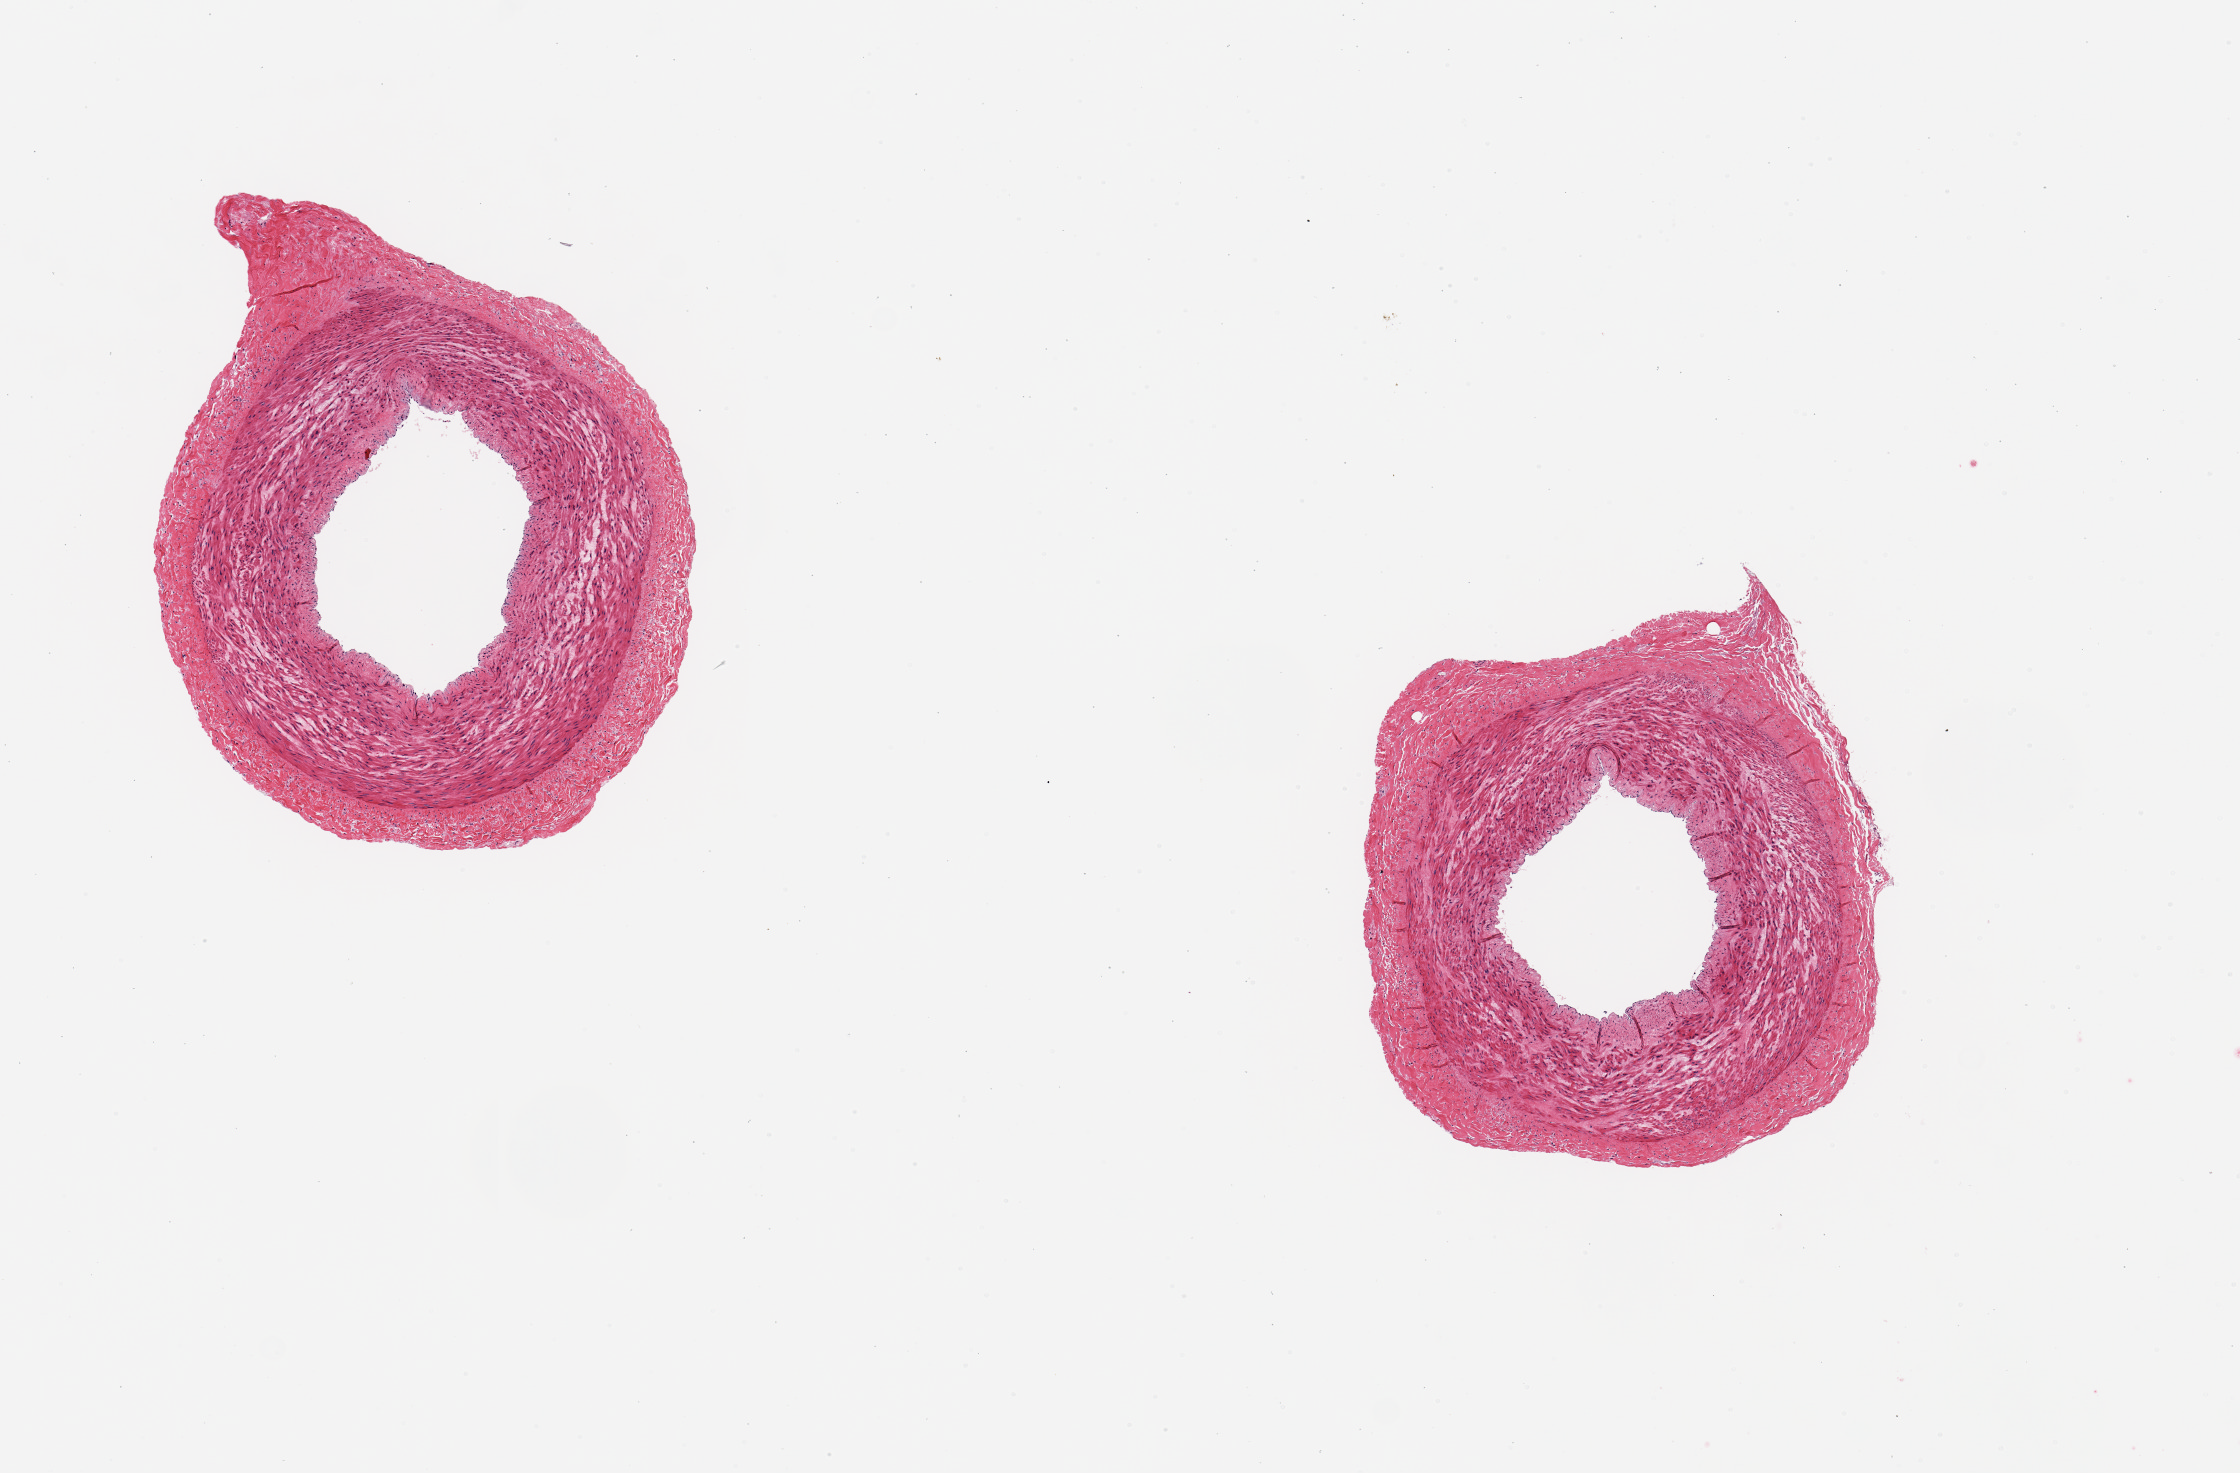
Digitized hematoxylin and eosin (H&E)-stained section, whole scanned area (about 8.9 x 5.8 mm) shown as a low-resolution overview, PAXgene-fixed, paraffin-embedded tissue, target tissue: tibial artery, donor tissue sample. Donor: female.
Pathologist's review note for this sample: 2 pieces, 2 mm diameter; no extraneous fat.